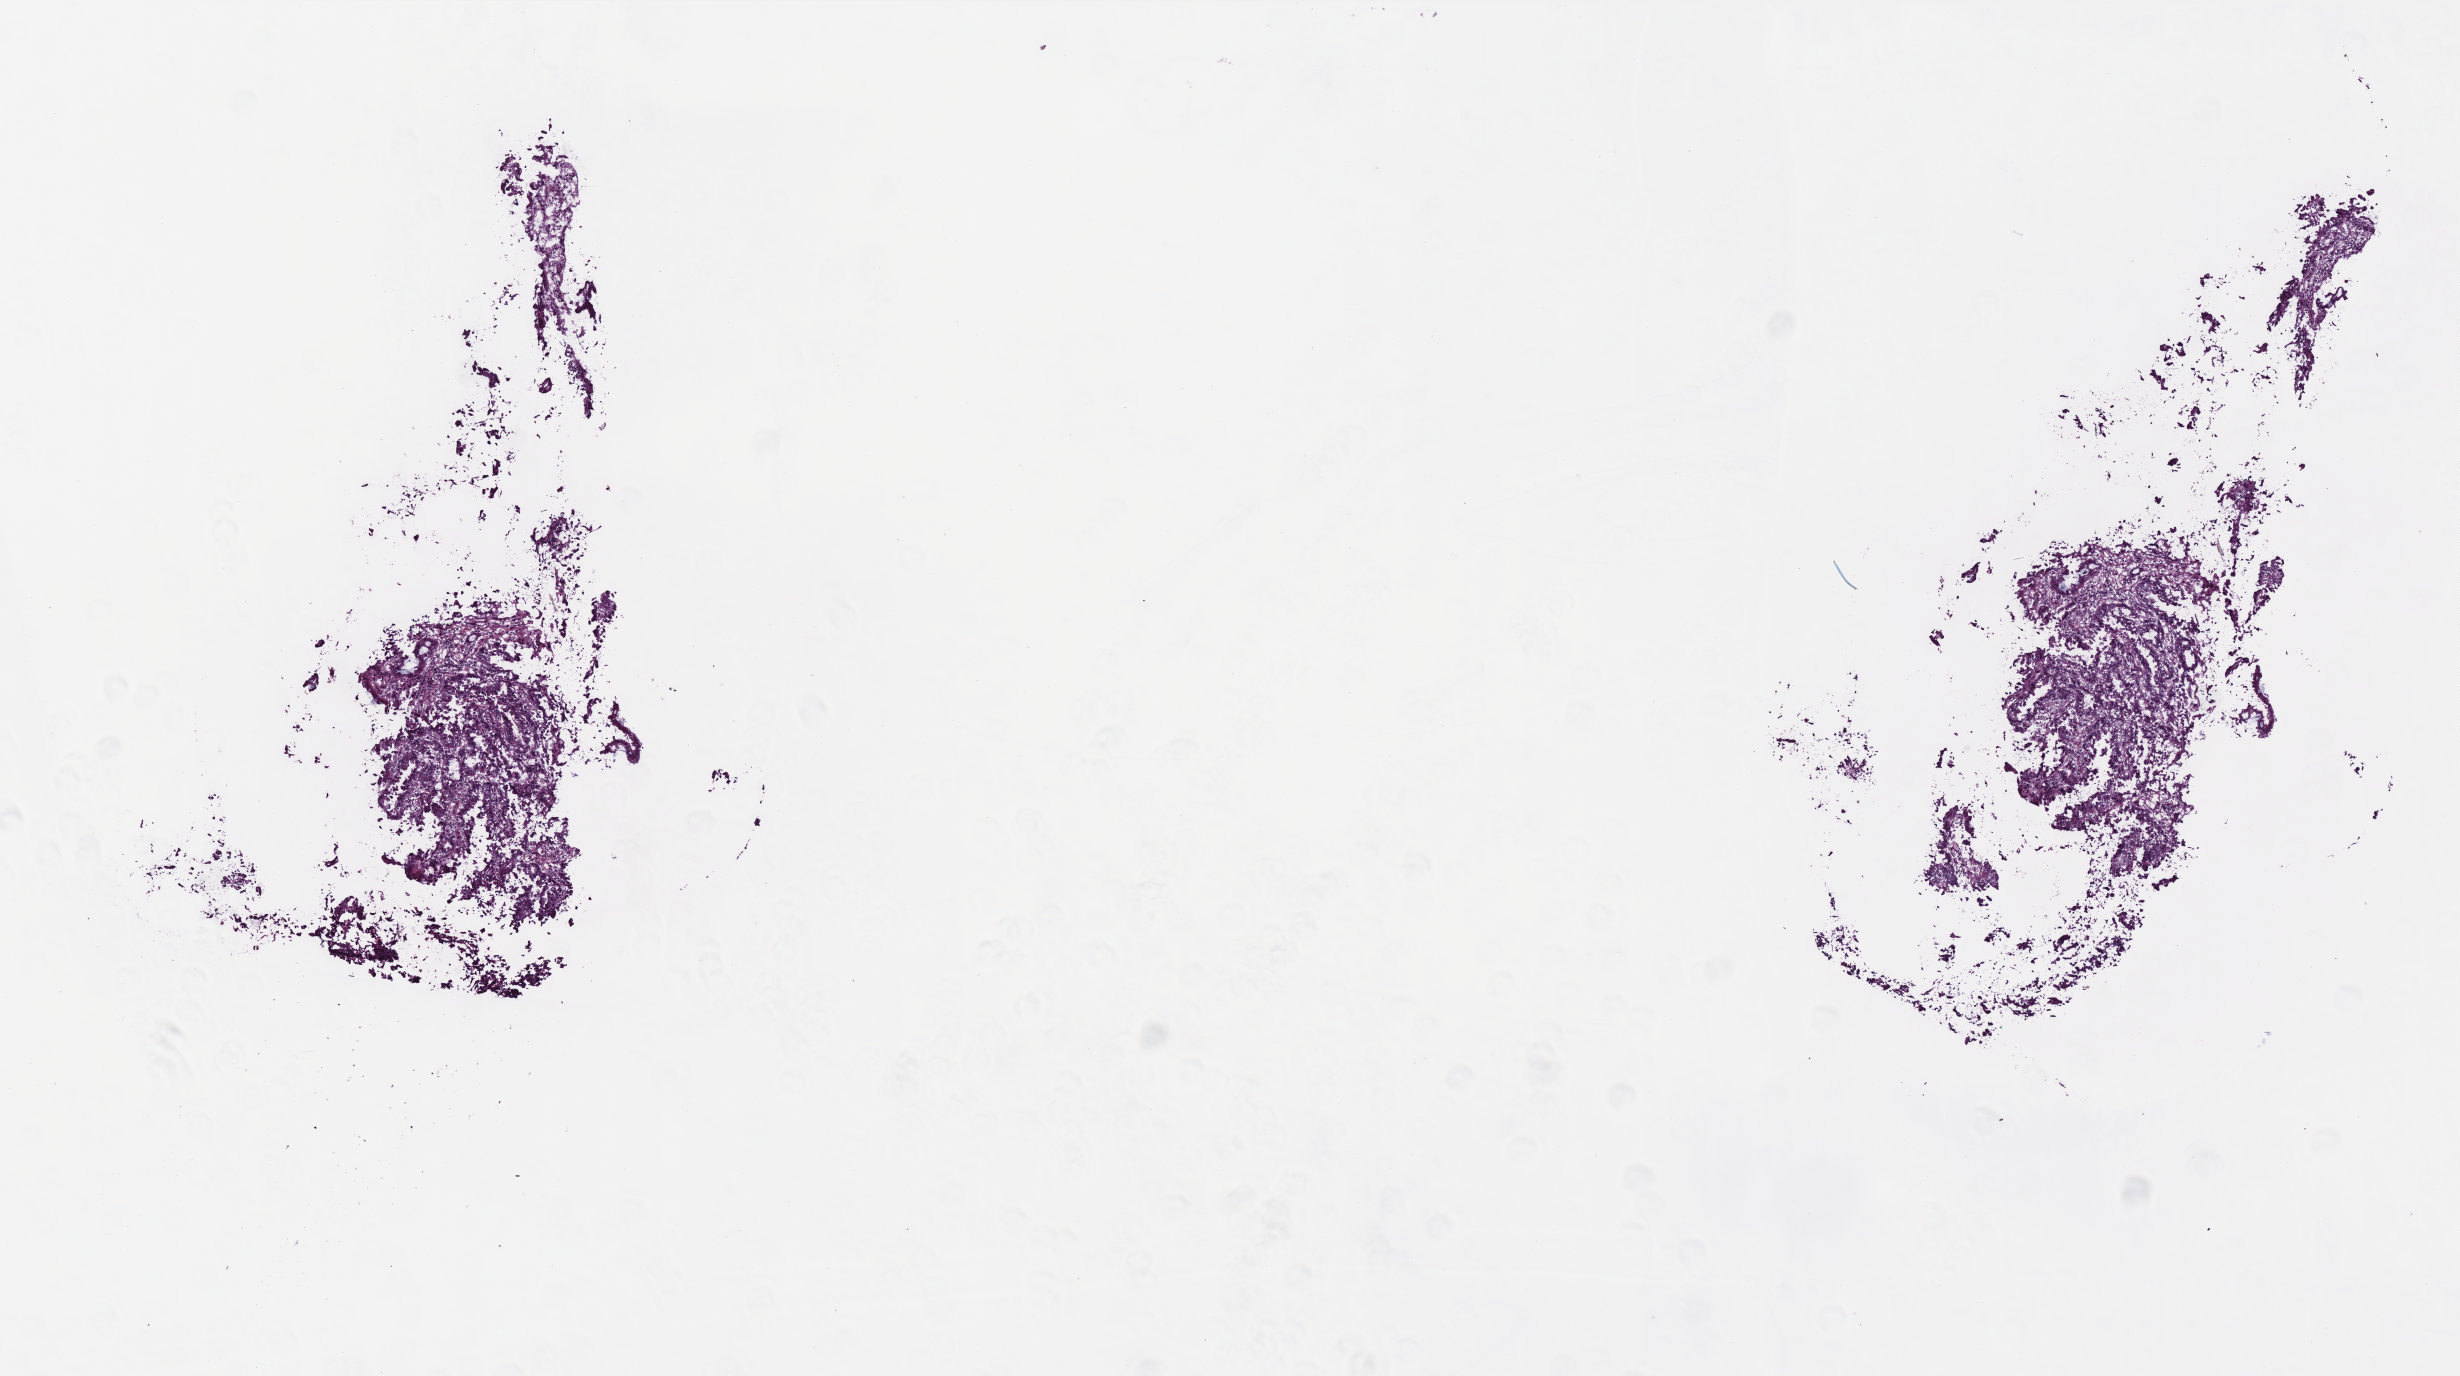
Whole-slide histology image, H&E-stained, shown as a low-resolution overview of the whole scanned area (about 9.9 x 5.5 mm, slide scanned at 40x), frozen section from the top of the tissue portion, sample: primary tumour, rectum. Female patient; age at initial diagnosis 49 years. Slide review estimates, as recorded: tumour cells 85%, tumour nuclei 85%, normal cells 0%, stromal cells 14%, necrosis 1%. Inflammatory infiltration, as recorded: lymphocyte infiltration 8%, monocyte infiltration 2%, neutrophil infiltration 1%.
AJCC pathologic stage: IIIB (6th edition). Lymph nodes positive (case pathology): 1 of 24 examined. Histologic diagnosis: Adenocarcinoma, NOS.